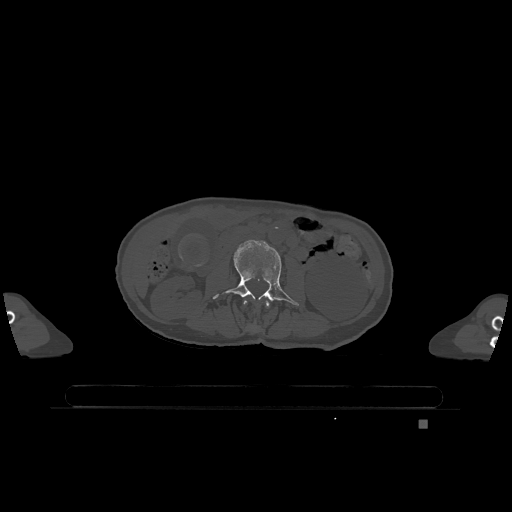
CT including the spine, one axial slice; position 362 of 1317 along the scan axis; bone window (W 1800 / L 400 HU); 0.5 mm slice thickness; 512 × 512 image matrix, field of view 500 × 500 mm. Patient: female, 74 years. Case-level facts recorded for this patient, not image findings: primary cancer: lung.
Outlined on this slice (semi-automatic segmentation, software-assisted and operator-edited):
- L2 vertebra: bounding box (x1, y1, x2, y2) in pixels: (243, 300, 270, 328)
- L3 vertebra: (213, 240, 299, 305)